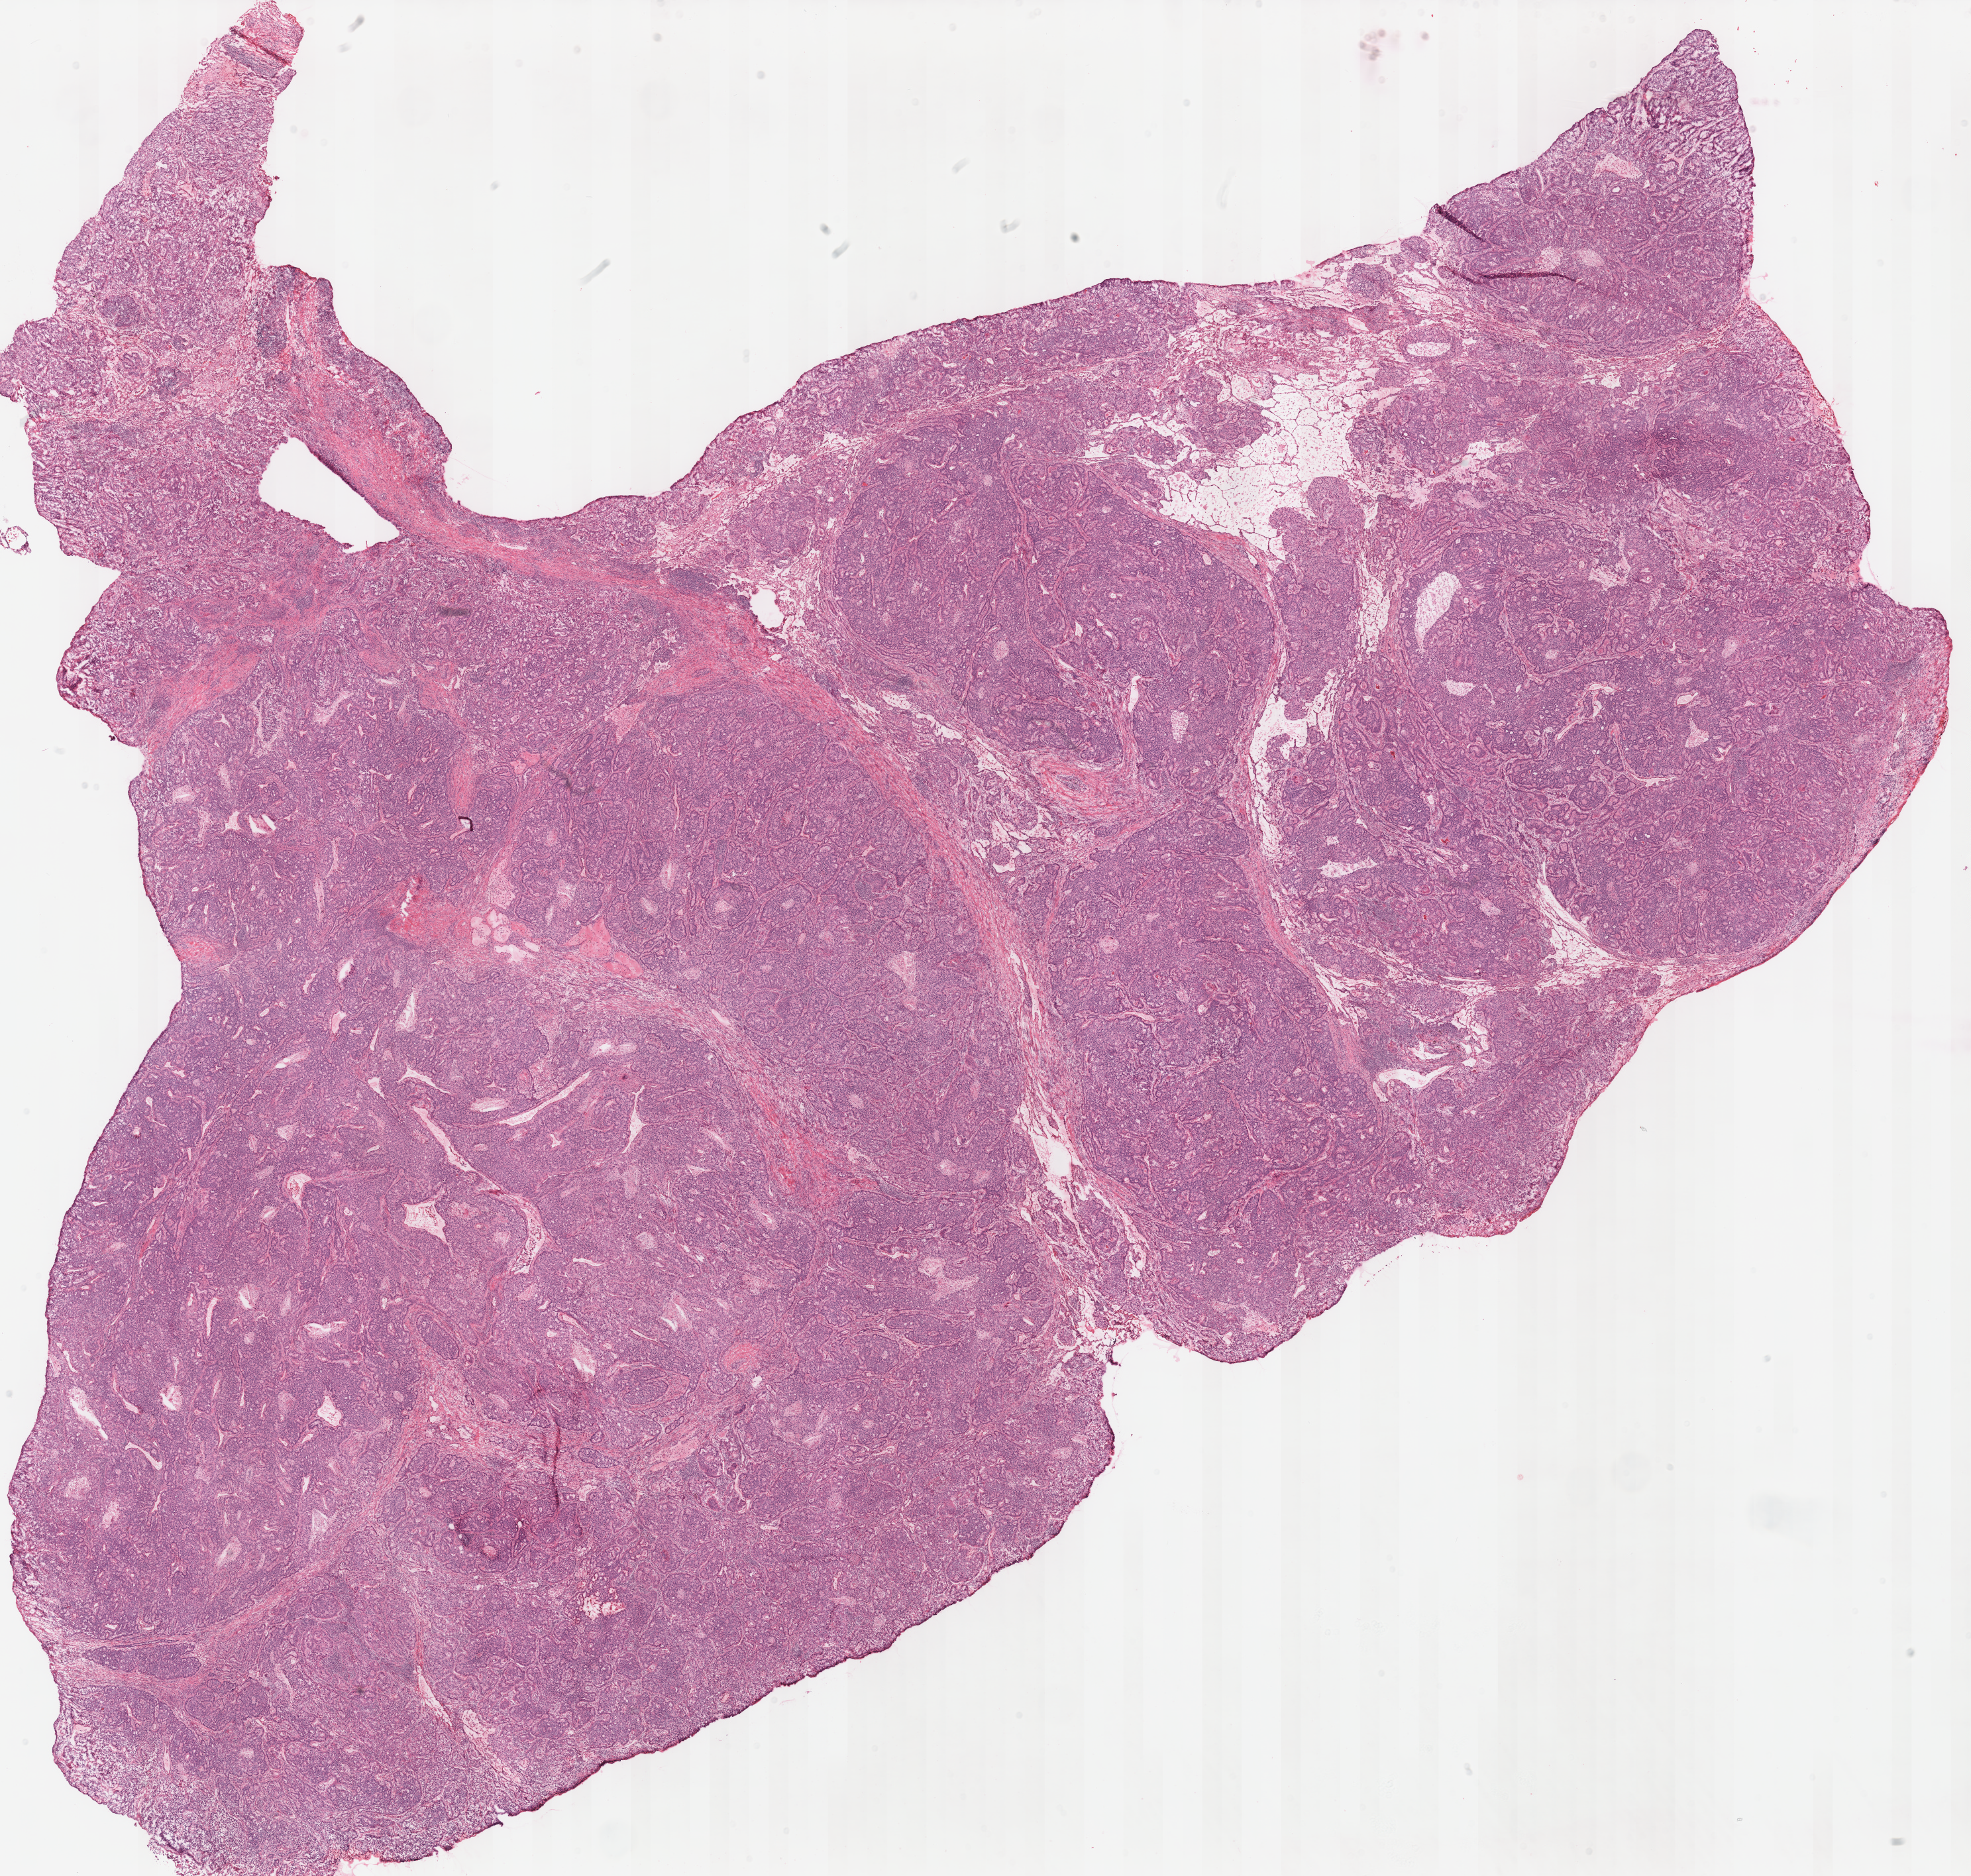
H&E-stained whole-slide image, shown as a low-resolution overview of the whole scanned area (about 23.4 x 22.3 mm, acquisition: 40x scan), frozen section from the top of the tissue portion, primary tumour sample from the lung. Patient: male, age at initial diagnosis 64 years. Composition of this section per pathologist review: tumour cells 100%, tumour nuclei 80%, normal cells 0%, stromal cells 0%, necrosis 0%. Infiltration values recorded for this section: lymphocyte infiltration 12%, monocyte infiltration 0%, neutrophil infiltration 0%.
Pathologic diagnosis: Adenocarcinoma, NOS (upper lobe, lung). AJCC pathologic stage: IA. Laterality: right.